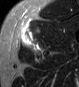
MRI of an extremity soft-tissue mass, one axial slice. Slice 38 of 45 in the series (ordered by position). STIR. MR volume resampled by the dataset authors to the PET/CT grid (not the native acquisition matrix). 3.27 mm slice thickness. 79 × 87 image matrix, field of view 77 × 85 mm. Male patient. From the clinical record (not read from this slice): histological type: pleiomorphic leiomyosarcoma; grade: high; site of the primary tumour: left thigh.
Structures marked on this image (expert contour drawn on MRI and transferred to this co-registered scan by the dataset authors):
- gross tumour volume including surrounding oedema: box from (x=22, y=29) to (x=39, y=51) px